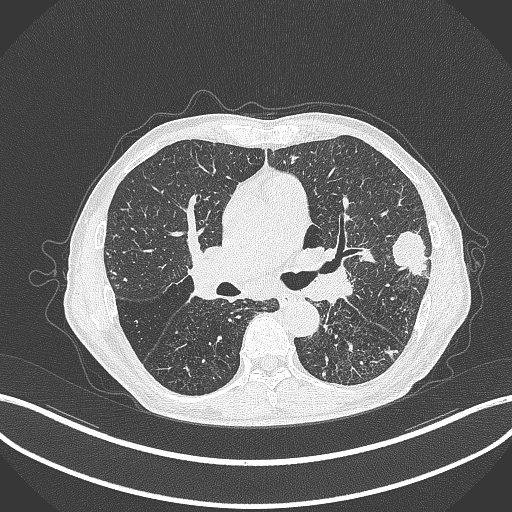
Chest CT, one axial slice. Reconstruction kernel B70f. Lung window (W 1500 / L -600 HU). 512 × 512 image matrix. Patient: male, 74 years. Case-level facts recorded for this patient, not image findings: clinical TNM (as recorded): T2a N1 M0.
Annotated regions visible in this slice (rectangle marked by the reading radiologist):
- lung tumour (recorded histology: adenocarcinoma): box from (x=386, y=225) to (x=430, y=283) px